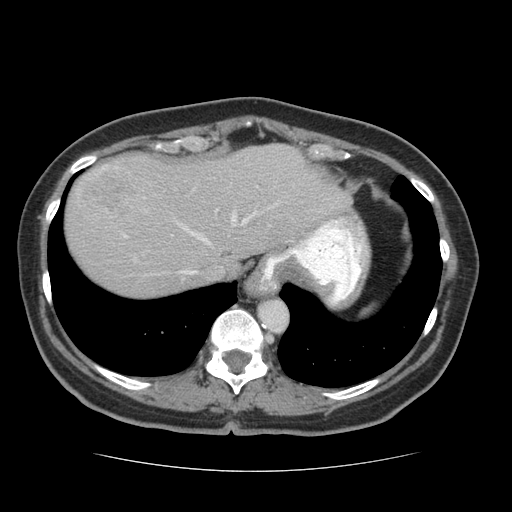
Contrast-enhanced abdominal CT (liver protocol), one axial slice. Reconstruction kernel STANDARD. 140 kVp. Soft-tissue window (W 400 / L 40 HU). 512 × 512 image matrix, field of view 360 × 360 mm. From the clinical record (not read from this slice): diagnosis: hepatocellular carcinoma (patient treated with transarterial chemoembolisation; whether this scan precedes or follows treatment is not stated here); TNM stage (as recorded): Stage-I; Child-Pugh class: A.
Structures marked on this image (semi-automatic segmentation, software-assisted and operator-edited):
- abdominal aorta: box from (x=259, y=300) to (x=288, y=331) px
- liver parenchyma outside the tumour (the mass and vessels are separate outlines, so this box may not span the whole liver): (x=64, y=144)–(x=350, y=296)
- mass: (x=80, y=163)–(x=138, y=215)
- liver vessels: (x=123, y=197)–(x=276, y=275)